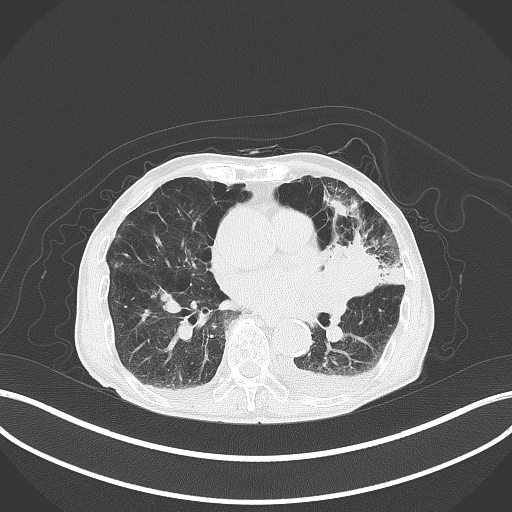
Chest CT, one axial slice. Slice 183 of 227 in the series (ordered by position). Lung window (W 1500 / L -600 HU). 3 mm slice thickness. 512 × 512 image matrix. Male patient, age 90 years or older. From the clinical record (not read from this slice): clinical TNM (as recorded): T2b N1 M0.
Annotated regions visible in this slice (bounding box drawn by a radiologist):
- lung tumour (recorded histology: squamous cell carcinoma): bounding box <317,239,404,302> (left, top, right, bottom; pixels)